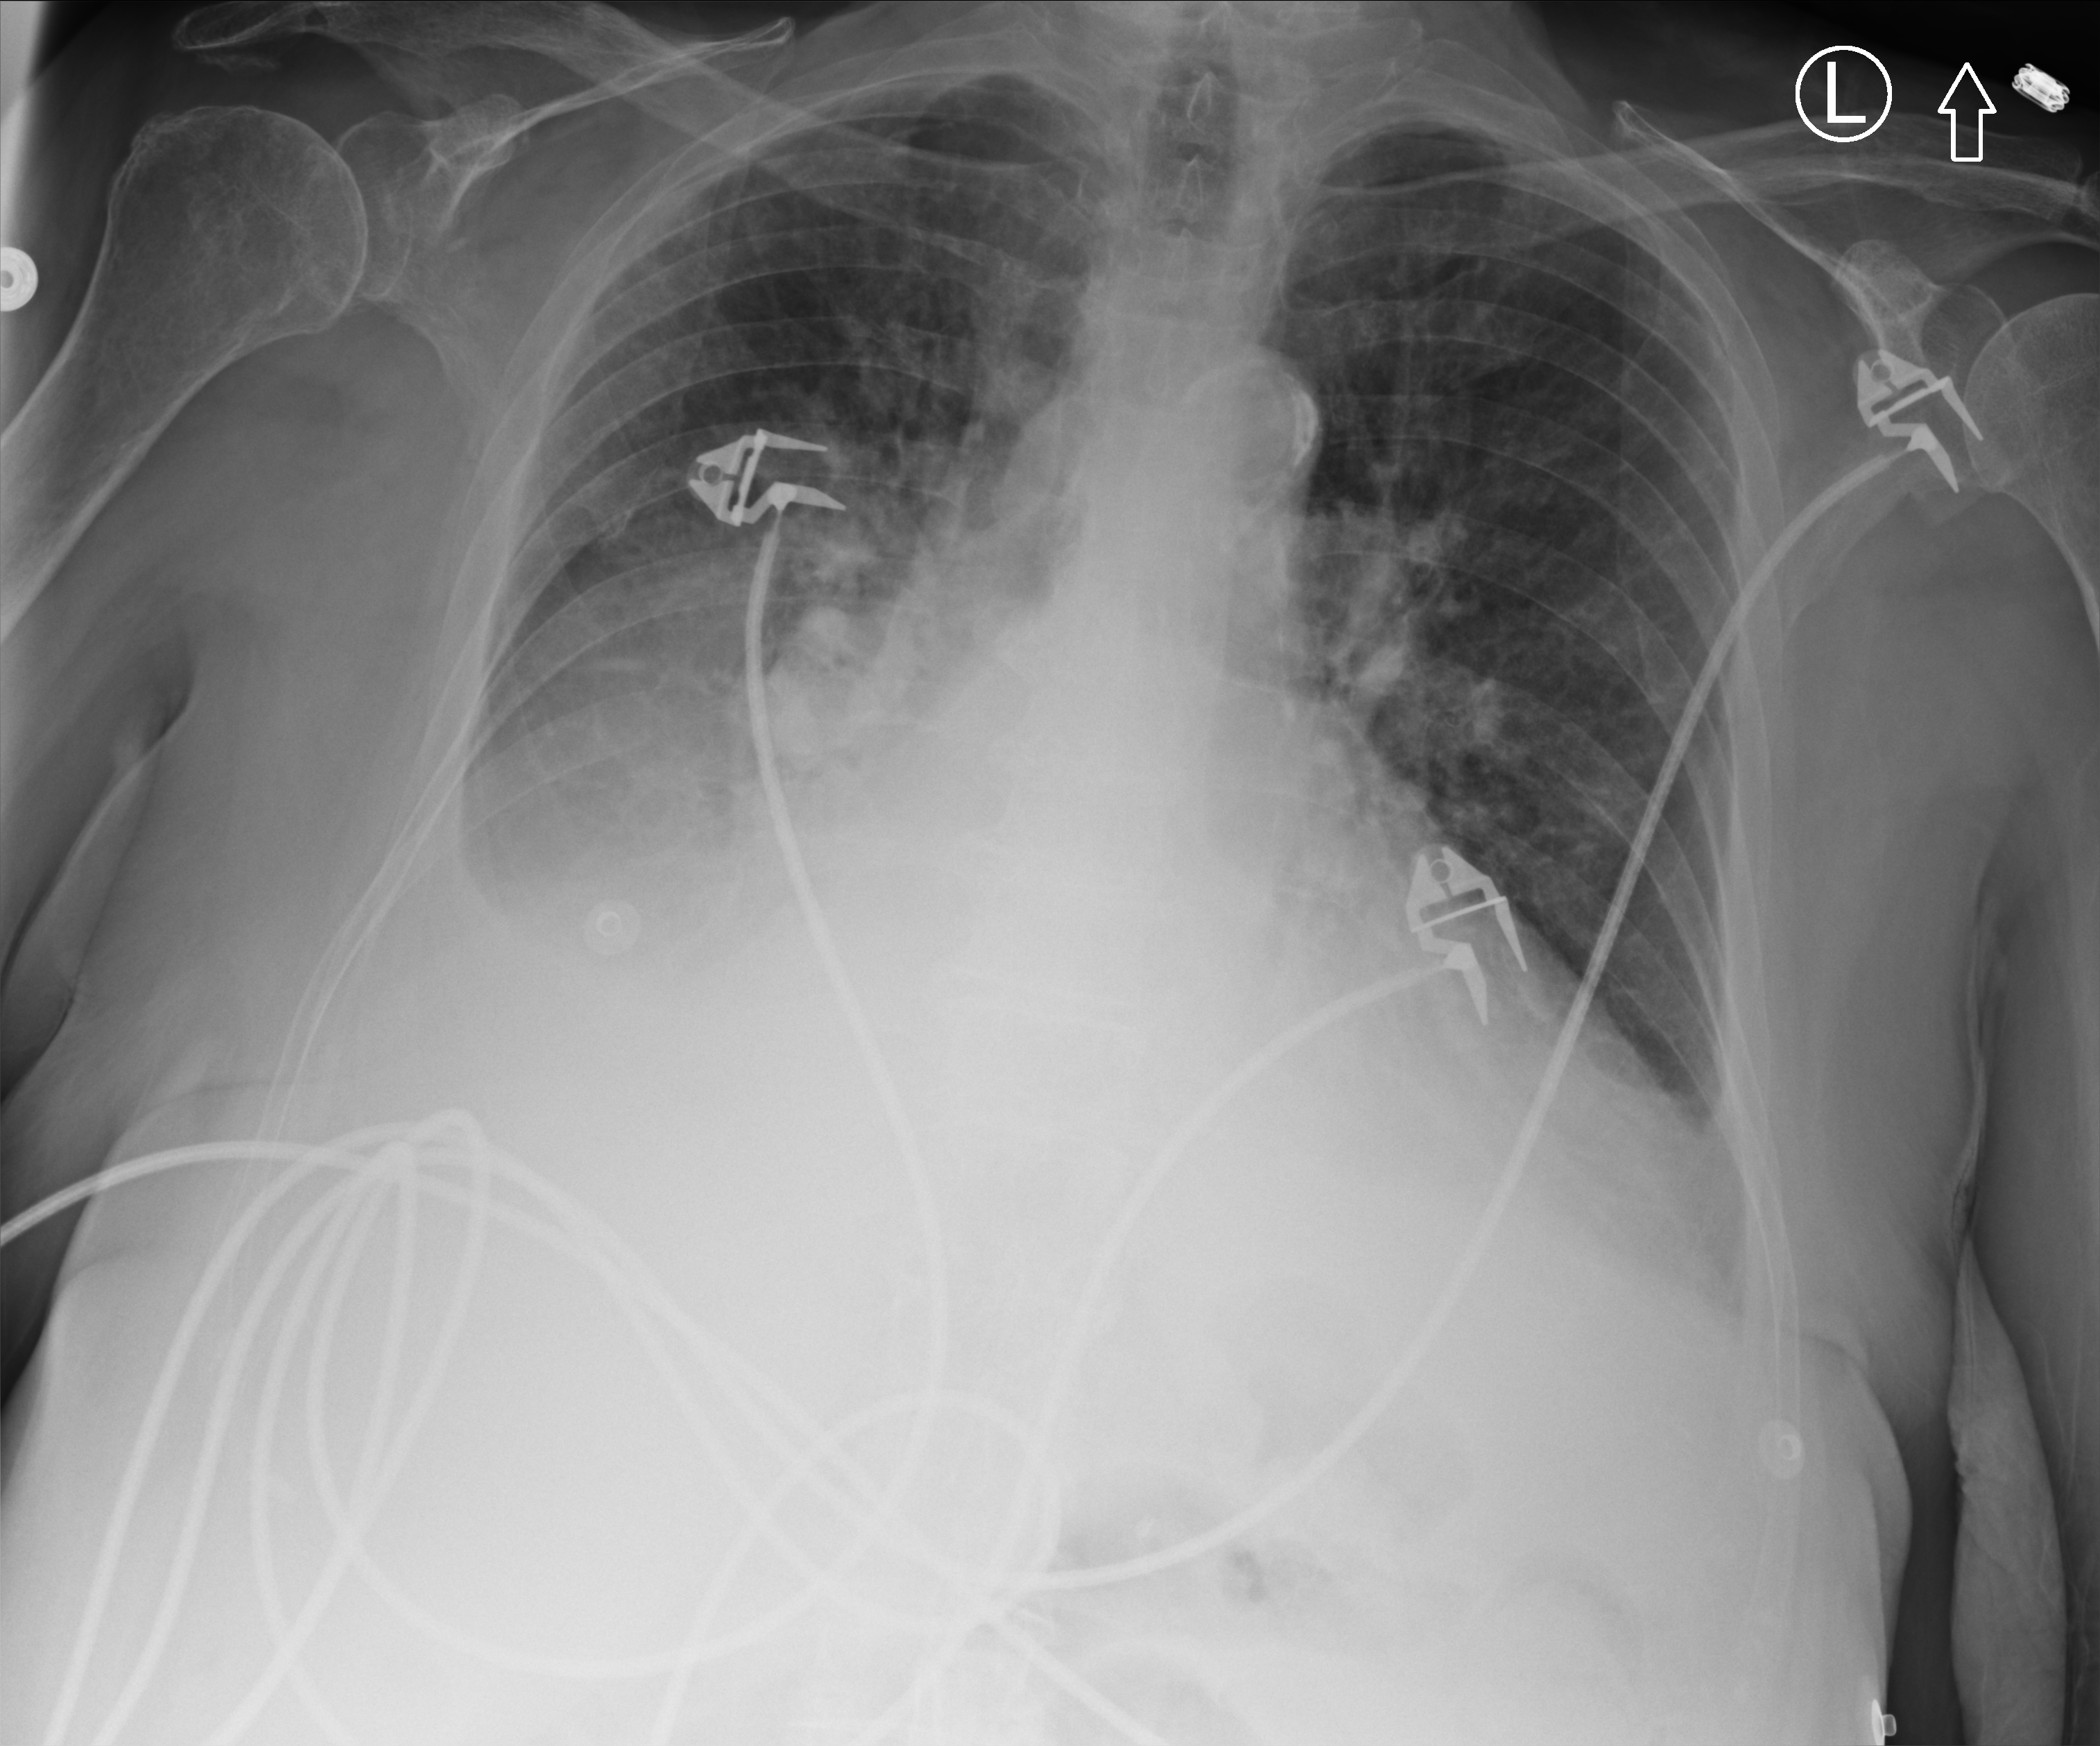
Bedside chest radiograph (computed radiography), anteroposterior (AP) projection. Patient hospitalised with COVID-19; female, aged 75–90 years.
Admission-level facts for this patient (not findings on this image; timing relative to this image not recorded): diabetes (admission record): no.